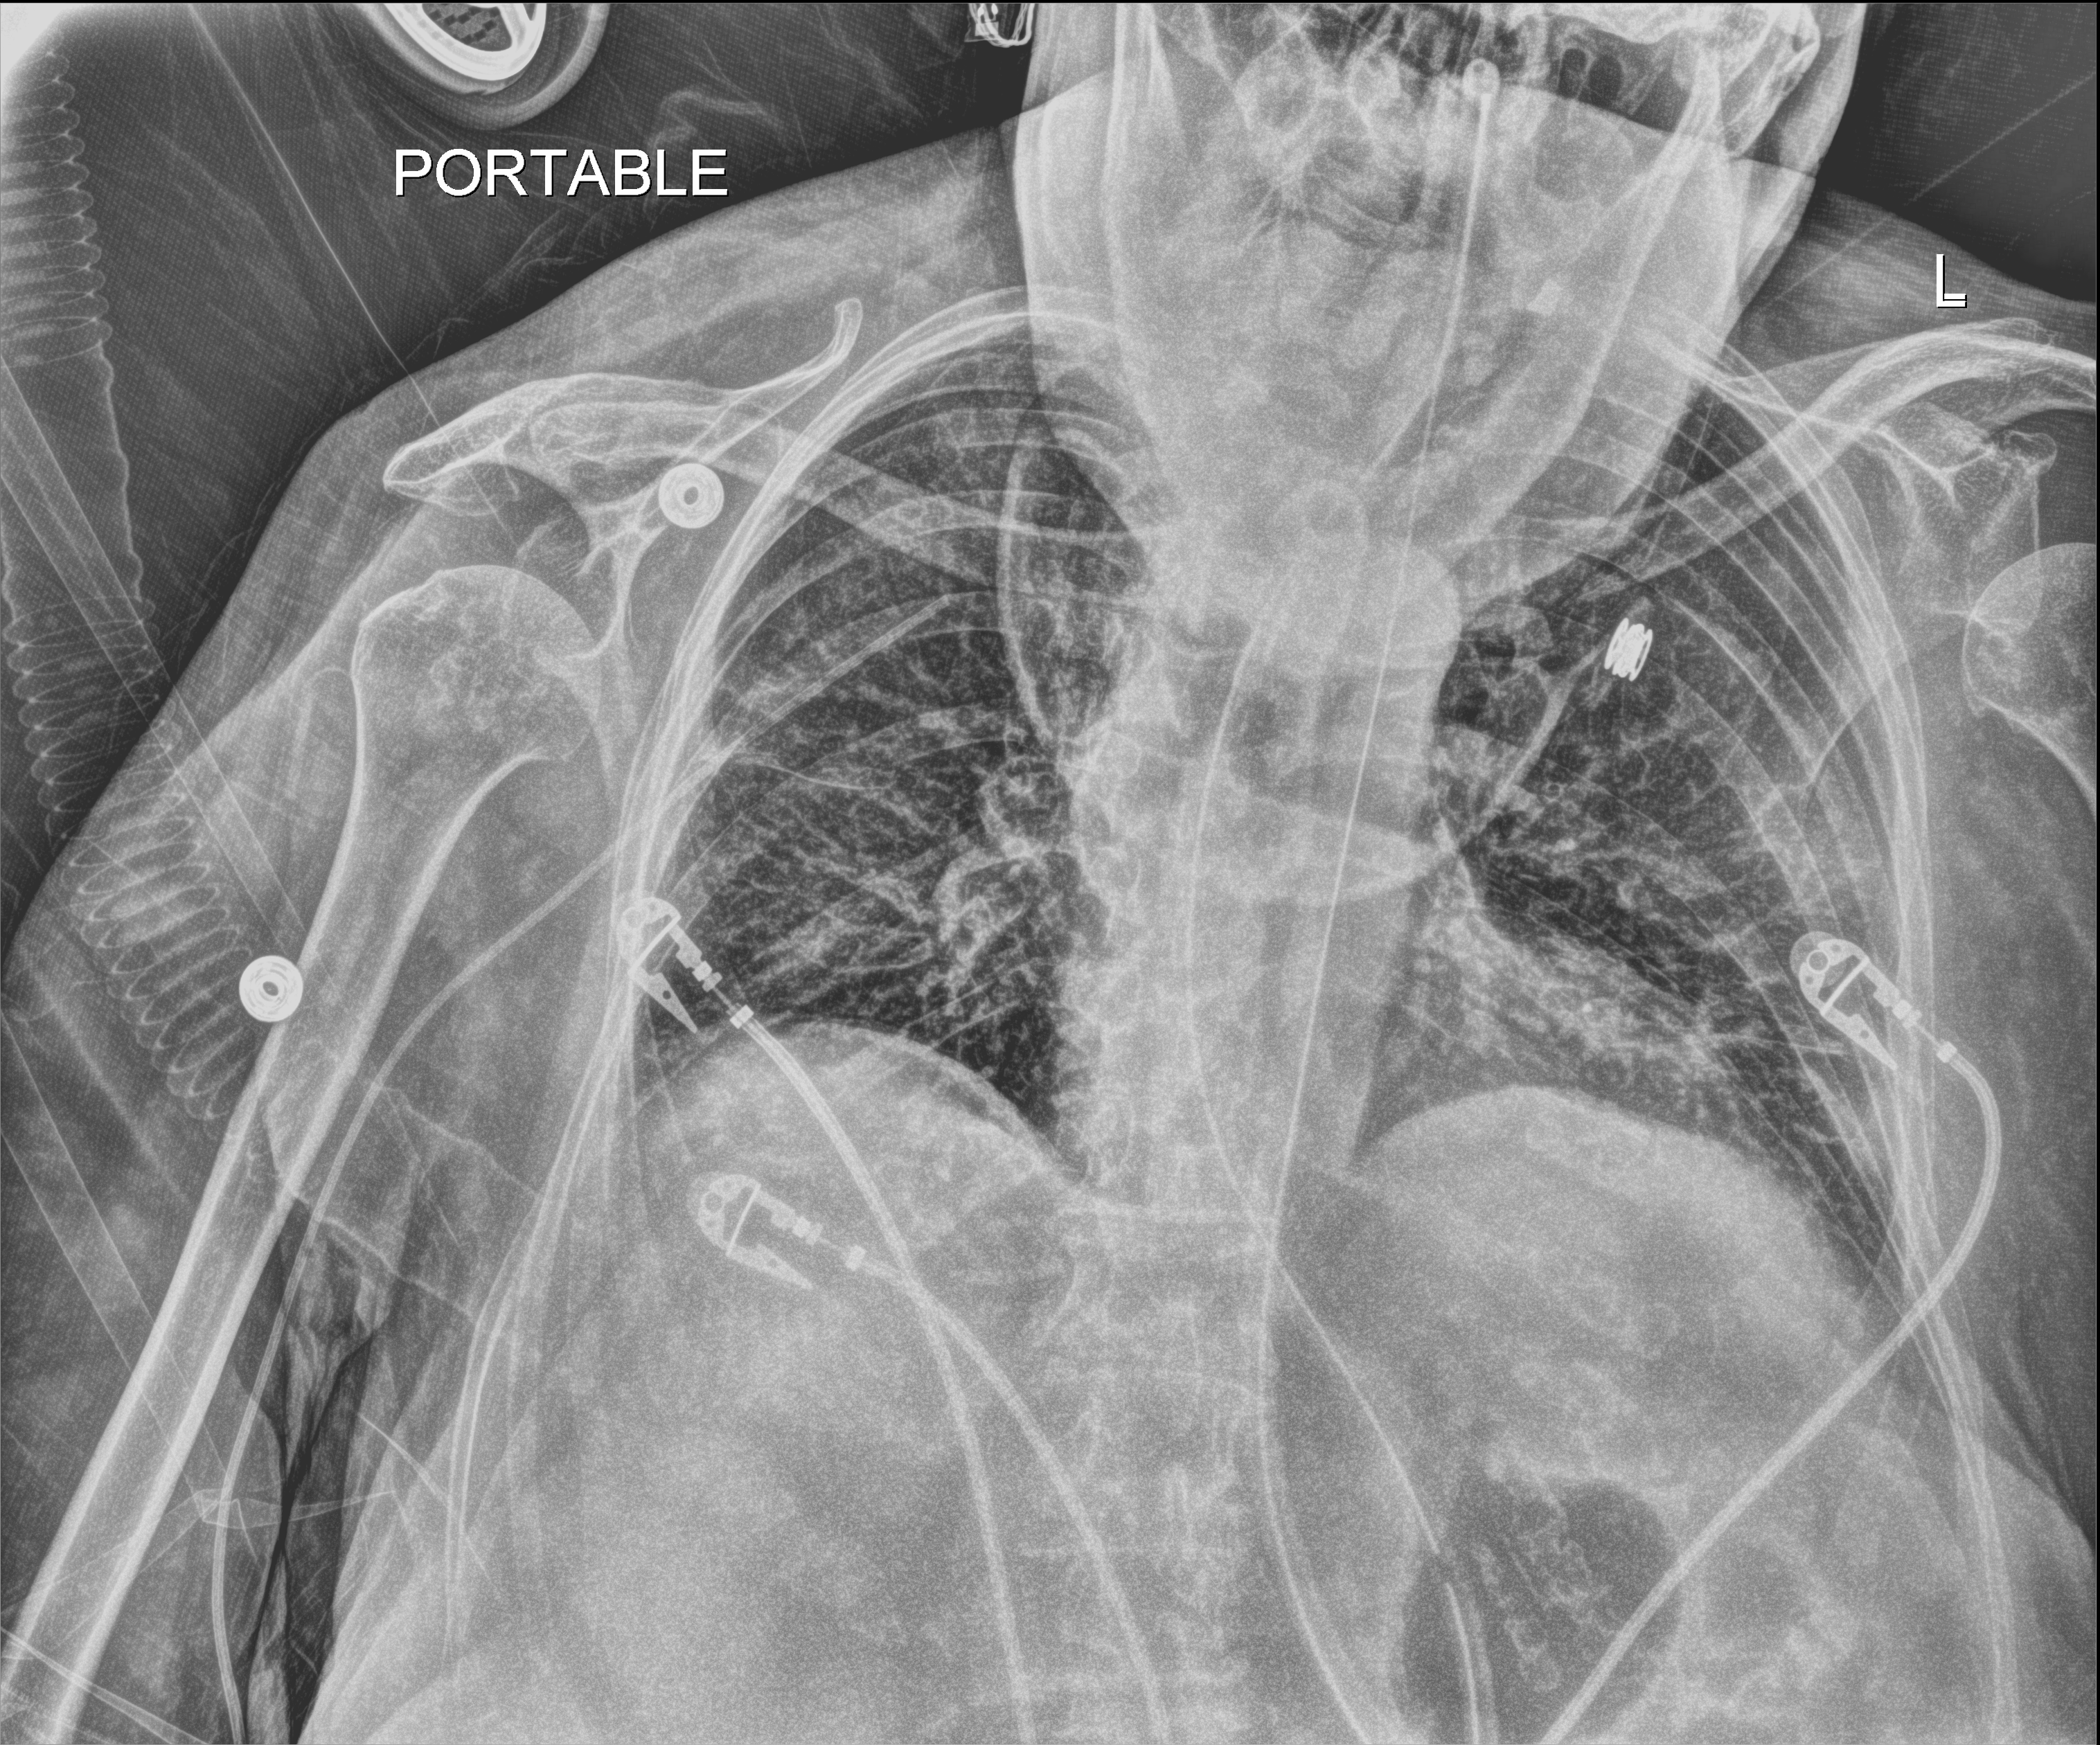
Bedside chest radiograph (digital radiography), anteroposterior (AP) projection. Female patient hospitalised with COVID-19, age 75–90 years.
Hospital-stay facts (about this admission, not read from this image; timing relative to this image not recorded): hypertension (admission record): yes.